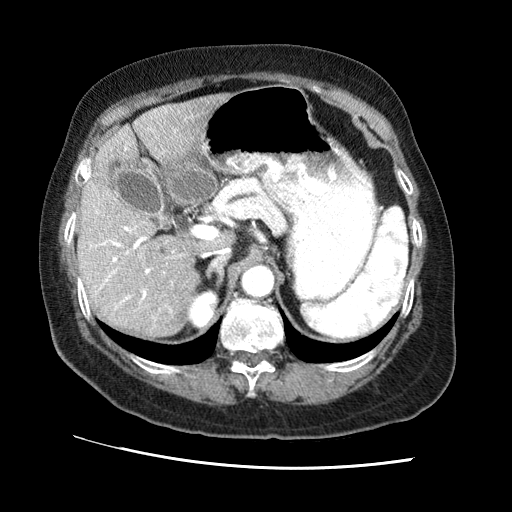
Contrast-enhanced abdominal CT (liver protocol), one axial slice; slice 38 of 65 in the series (ordered by position); reconstruction kernel STANDARD; 120 kVp; soft-tissue window (W 400 / L 40 HU); 2.5 mm slice thickness; 512 × 512 image matrix, field of view 340 × 340 mm. Case-level facts recorded for this patient, not image findings: diagnosis: hepatocellular carcinoma (patient treated with transarterial chemoembolisation; whether this scan precedes or follows treatment is not stated here); TNM stage (as recorded): Stage-II; Child-Pugh class: A; tumour nodularity: multinodular; tumour size: 2.5 cm.
Annotated regions visible in this slice (semi-automatic segmentation, software-assisted and operator-edited):
- liver parenchyma outside the tumour (the mass and vessels are separate outlines, so this box may not span the whole liver): bounding box [x1, y1, x2, y2] px = [78, 94, 228, 338]
- liver vessels: [95, 146, 174, 319]